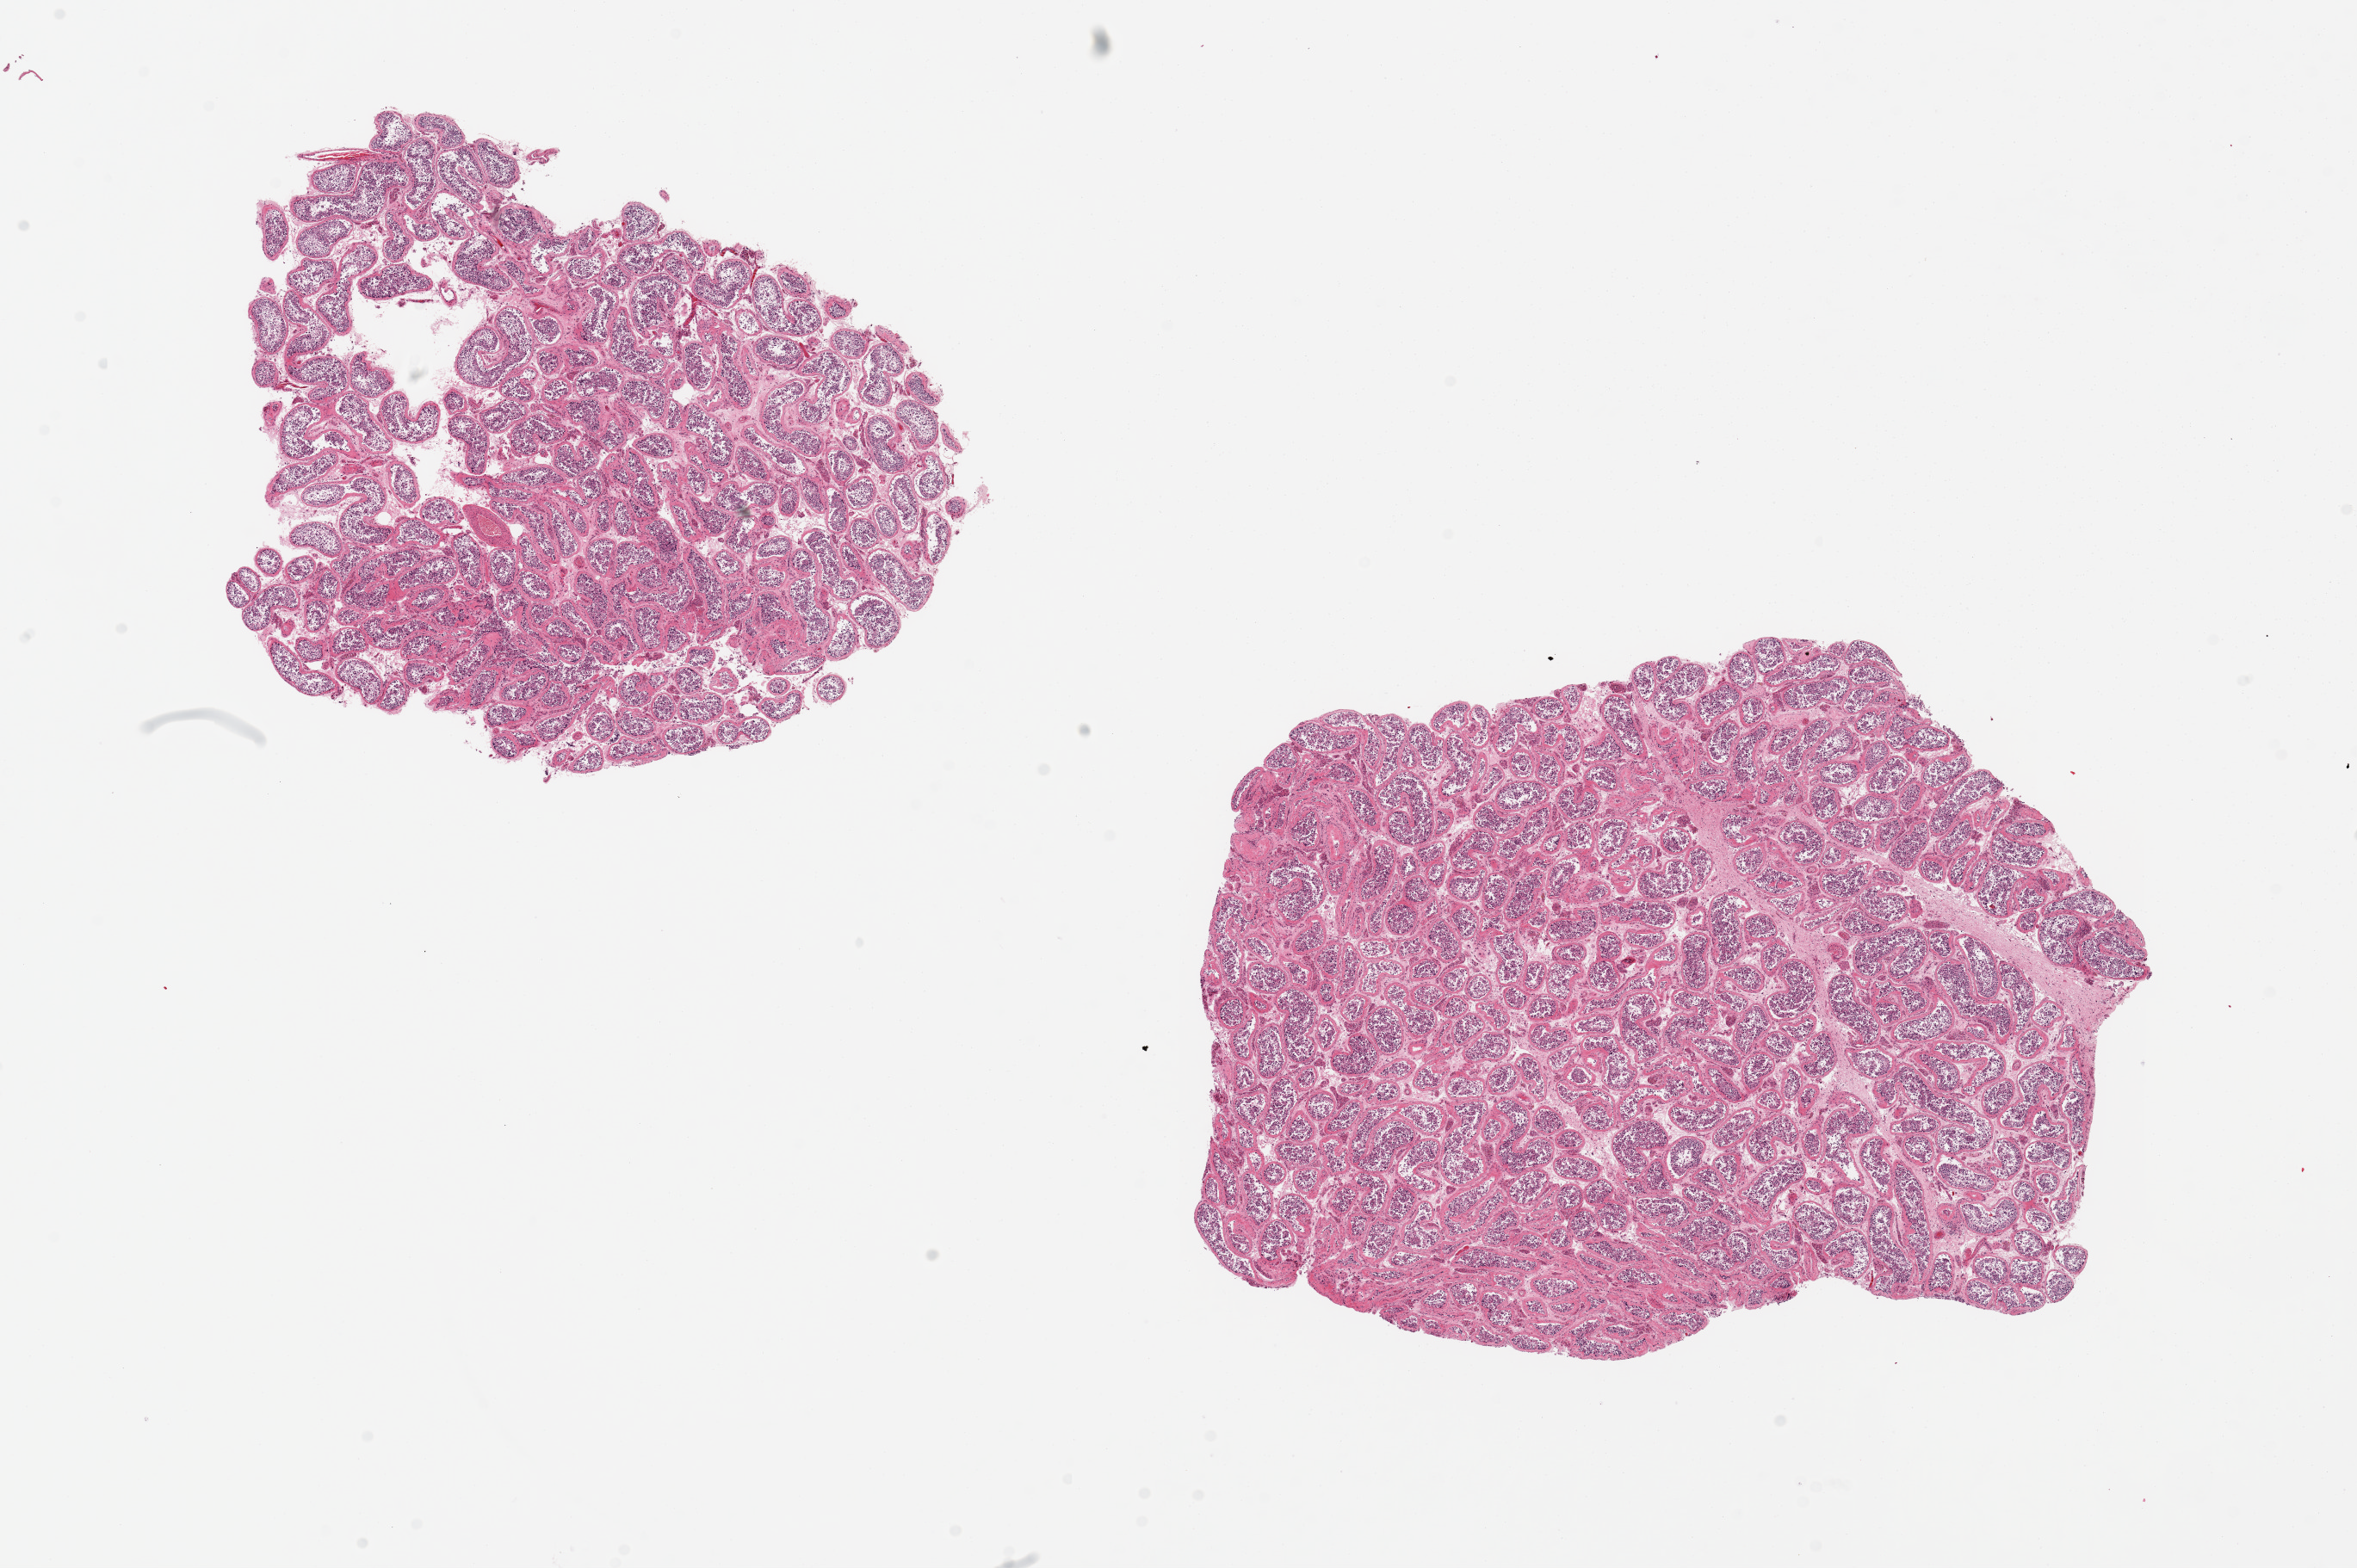
Digitized haematoxylin and eosin-stained section — whole scanned area (about 21.7 x 14.4 mm, from a 20x scan) shown as a low-resolution overview. PAXgene-fixed, paraffin-embedded tissue. Section of testis (target tissue). Tissue donor sample. Donor: male.
* review note (as recorded): 2 pieces. 7x5 & 9x7mm; spermatogenesiis present but poorly preserved